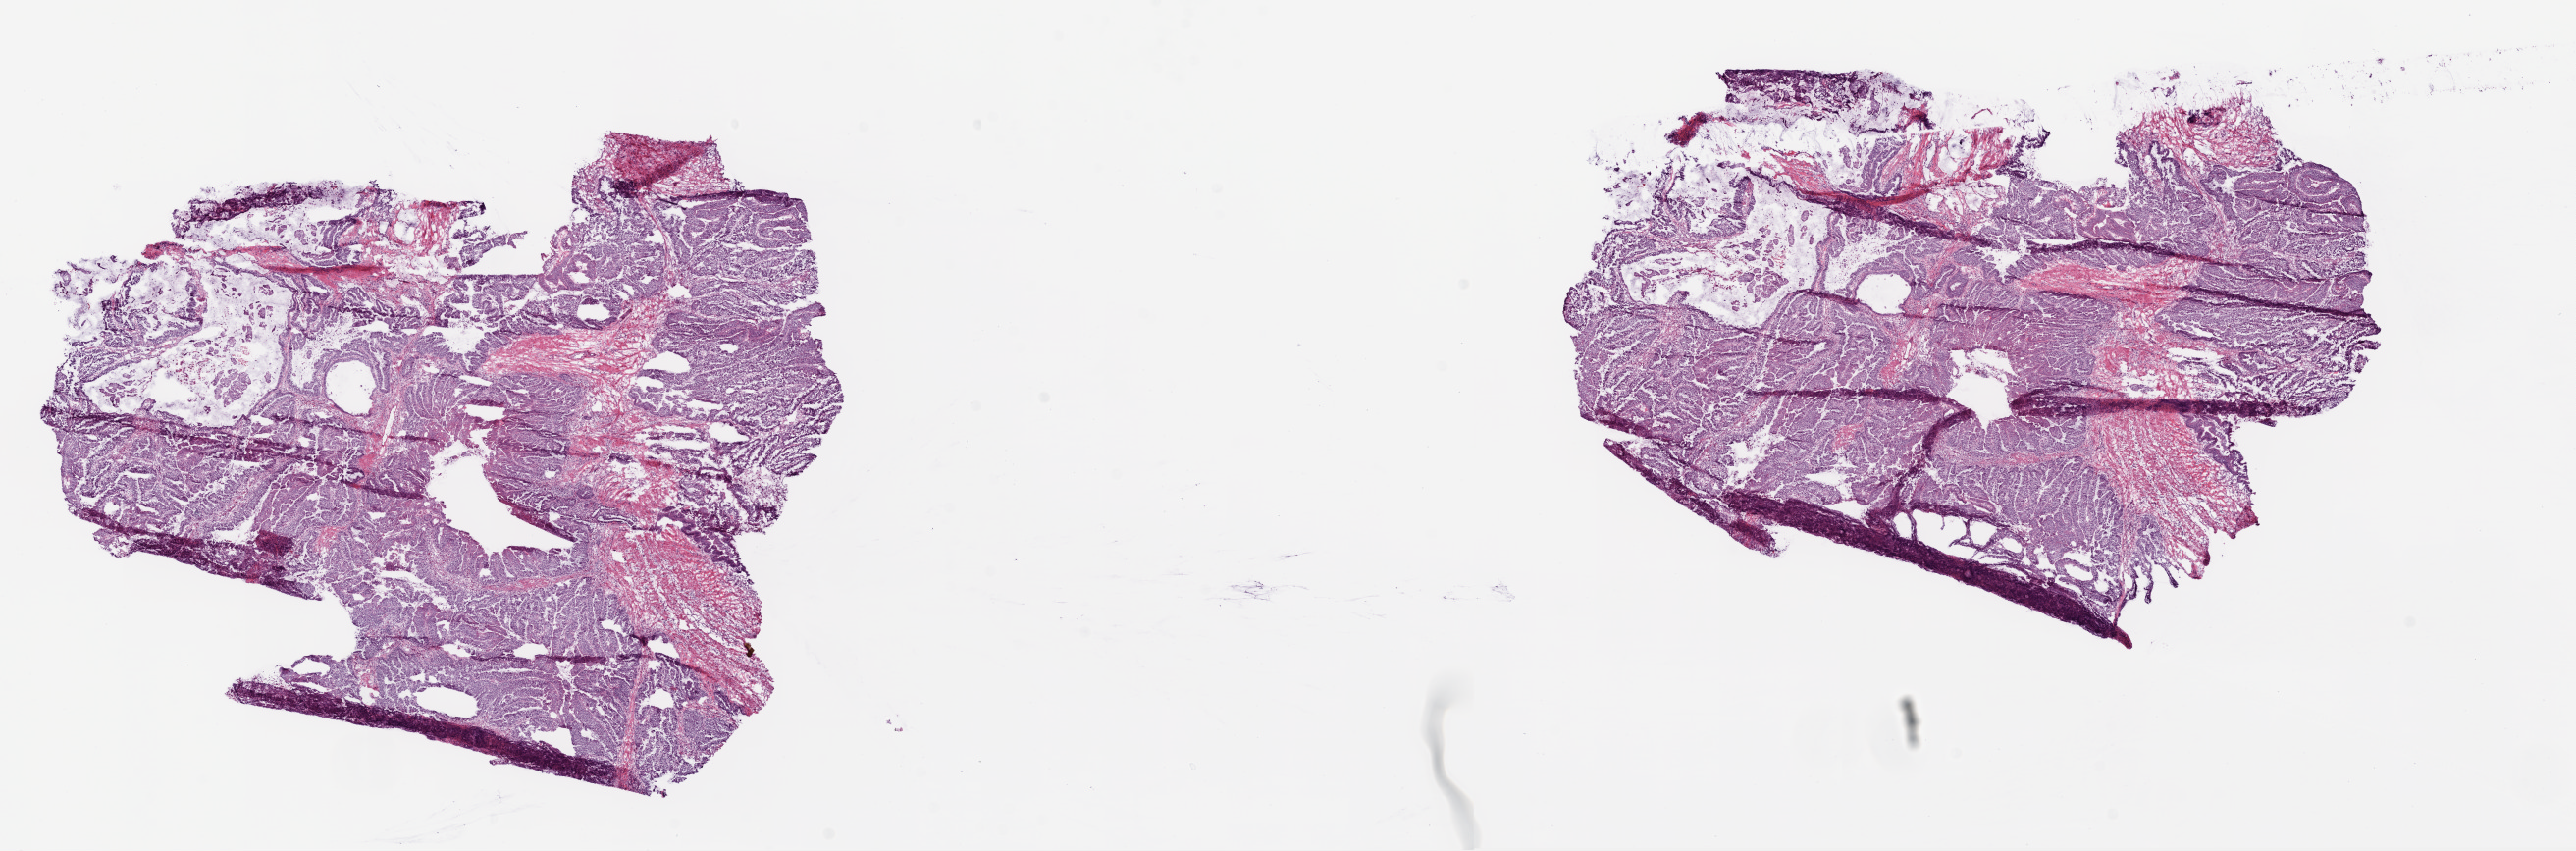
Whole-slide histology image, H&E, a low-resolution overview of the entire scanned area, about 21.1 x 7.0 mm. Frozen section. Primary tumour sample from the colon. Male, age 69 years at initial diagnosis. Composition of this section per pathologist review: tumour cells 80%, tumour nuclei 96%, normal cells 15%, stromal cells 5%, necrosis 0%.
- pathologic diagnosis: Mucinous adenocarcinoma
- AJCC pathologic stage: IIIB
- lymph nodes positive (case pathology): 2 of 24 examined